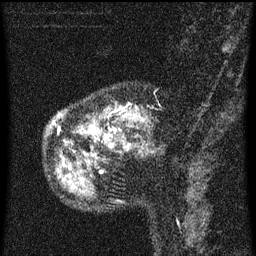
Breast MRI (dynamic contrast-enhanced), one sagittal slice. Position 17 of 60 along the scan axis. Dynamic contrast-enhanced series, image 2 of 3 at this slice position (ordered by acquisition). 1.5 T. TE 4.2 ms, TR 8 ms. 2 mm slice thickness. 256 × 256 image matrix, field of view 180 × 180 mm. Patient: female, 55 years.
Structures marked on this image (semi-automatic segmentation, software-assisted and operator-edited):
- analysis volume of interest (the breast-tissue region the enhancement analysis was run in; not a lesion): bounding box [x1, y1, x2, y2] px = [44, 84, 159, 155]
- tumour enhancement mask (voxels above the 70 % enhancement threshold inside the analysis volume of interest): [58, 104, 146, 141]